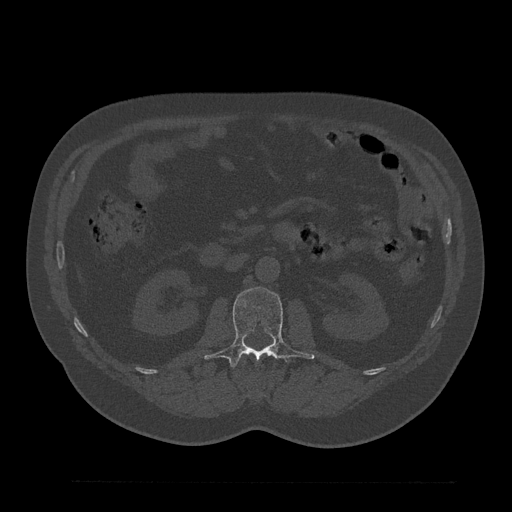
CT including the spine, one axial slice. Slice 108 of 797 in the series (ordered by position). 120 kVp. Bone window (W 1800 / L 400 HU). 0.5 mm slice thickness. 512 × 512 image matrix. Male patient, age 61 years. Case-level facts recorded for this patient, not image findings: primary cancer: prostate.
Annotated regions visible in this slice (semi-automatic segmentation, software-assisted and operator-edited):
- L1 vertebra: bounding box (x1, y1, x2, y2) in pixels: (243, 352, 272, 364)
- L2 vertebra: (205, 287, 315, 370)